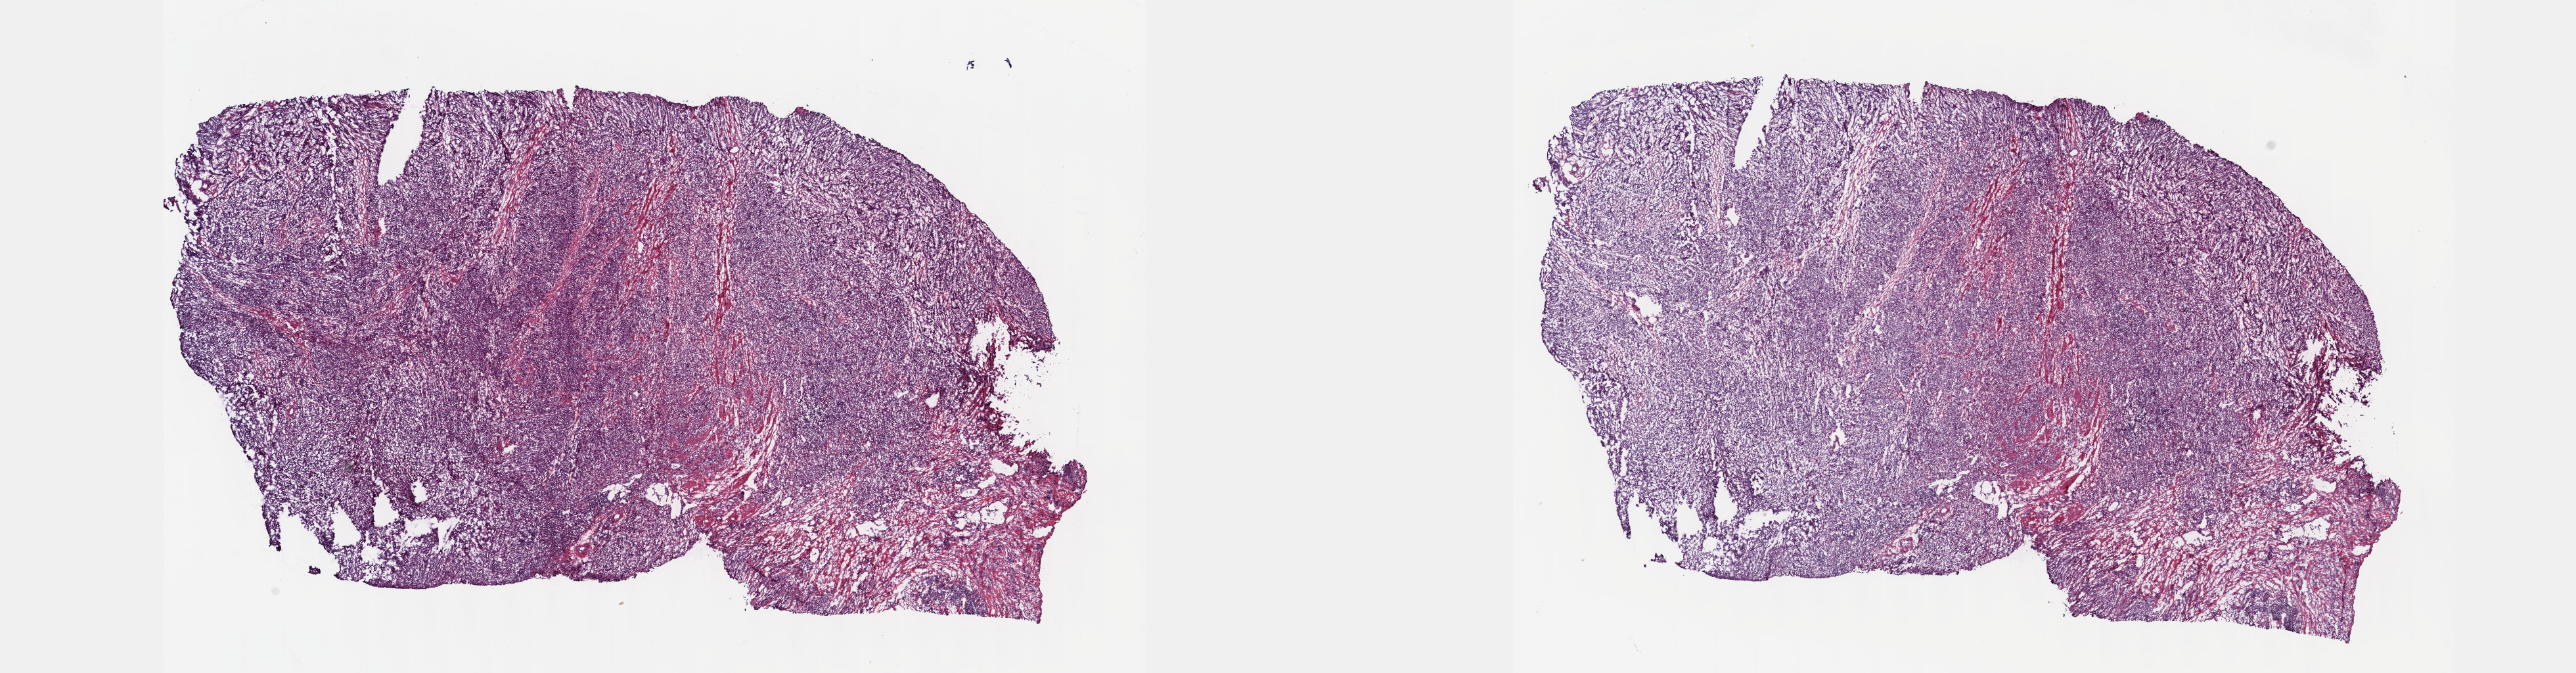
Whole-slide histology image, H&E, shown as a low-resolution overview of the whole scanned area (about 31.7 x 8.3 mm), frozen section from the top of the tissue portion, esophagus, primary tumour sample. Patient: male, age at initial diagnosis 60 years. Histologic grade: G3 (poorly differentiated). Slide review estimates, as recorded: tumour cells 100%, tumour nuclei 90%, normal cells 0%, stromal cells 0%, necrosis 0%. Inflammatory infiltration, as recorded: lymphocyte infiltration 0%, monocyte infiltration 0%, neutrophil infiltration 0%.
- pathologic diagnosis: Squamous cell carcinoma, NOS (lower third of esophagus)
- AJCC pathologic stage: IIIA (7th edition)
- TNM: T3 N1 M0